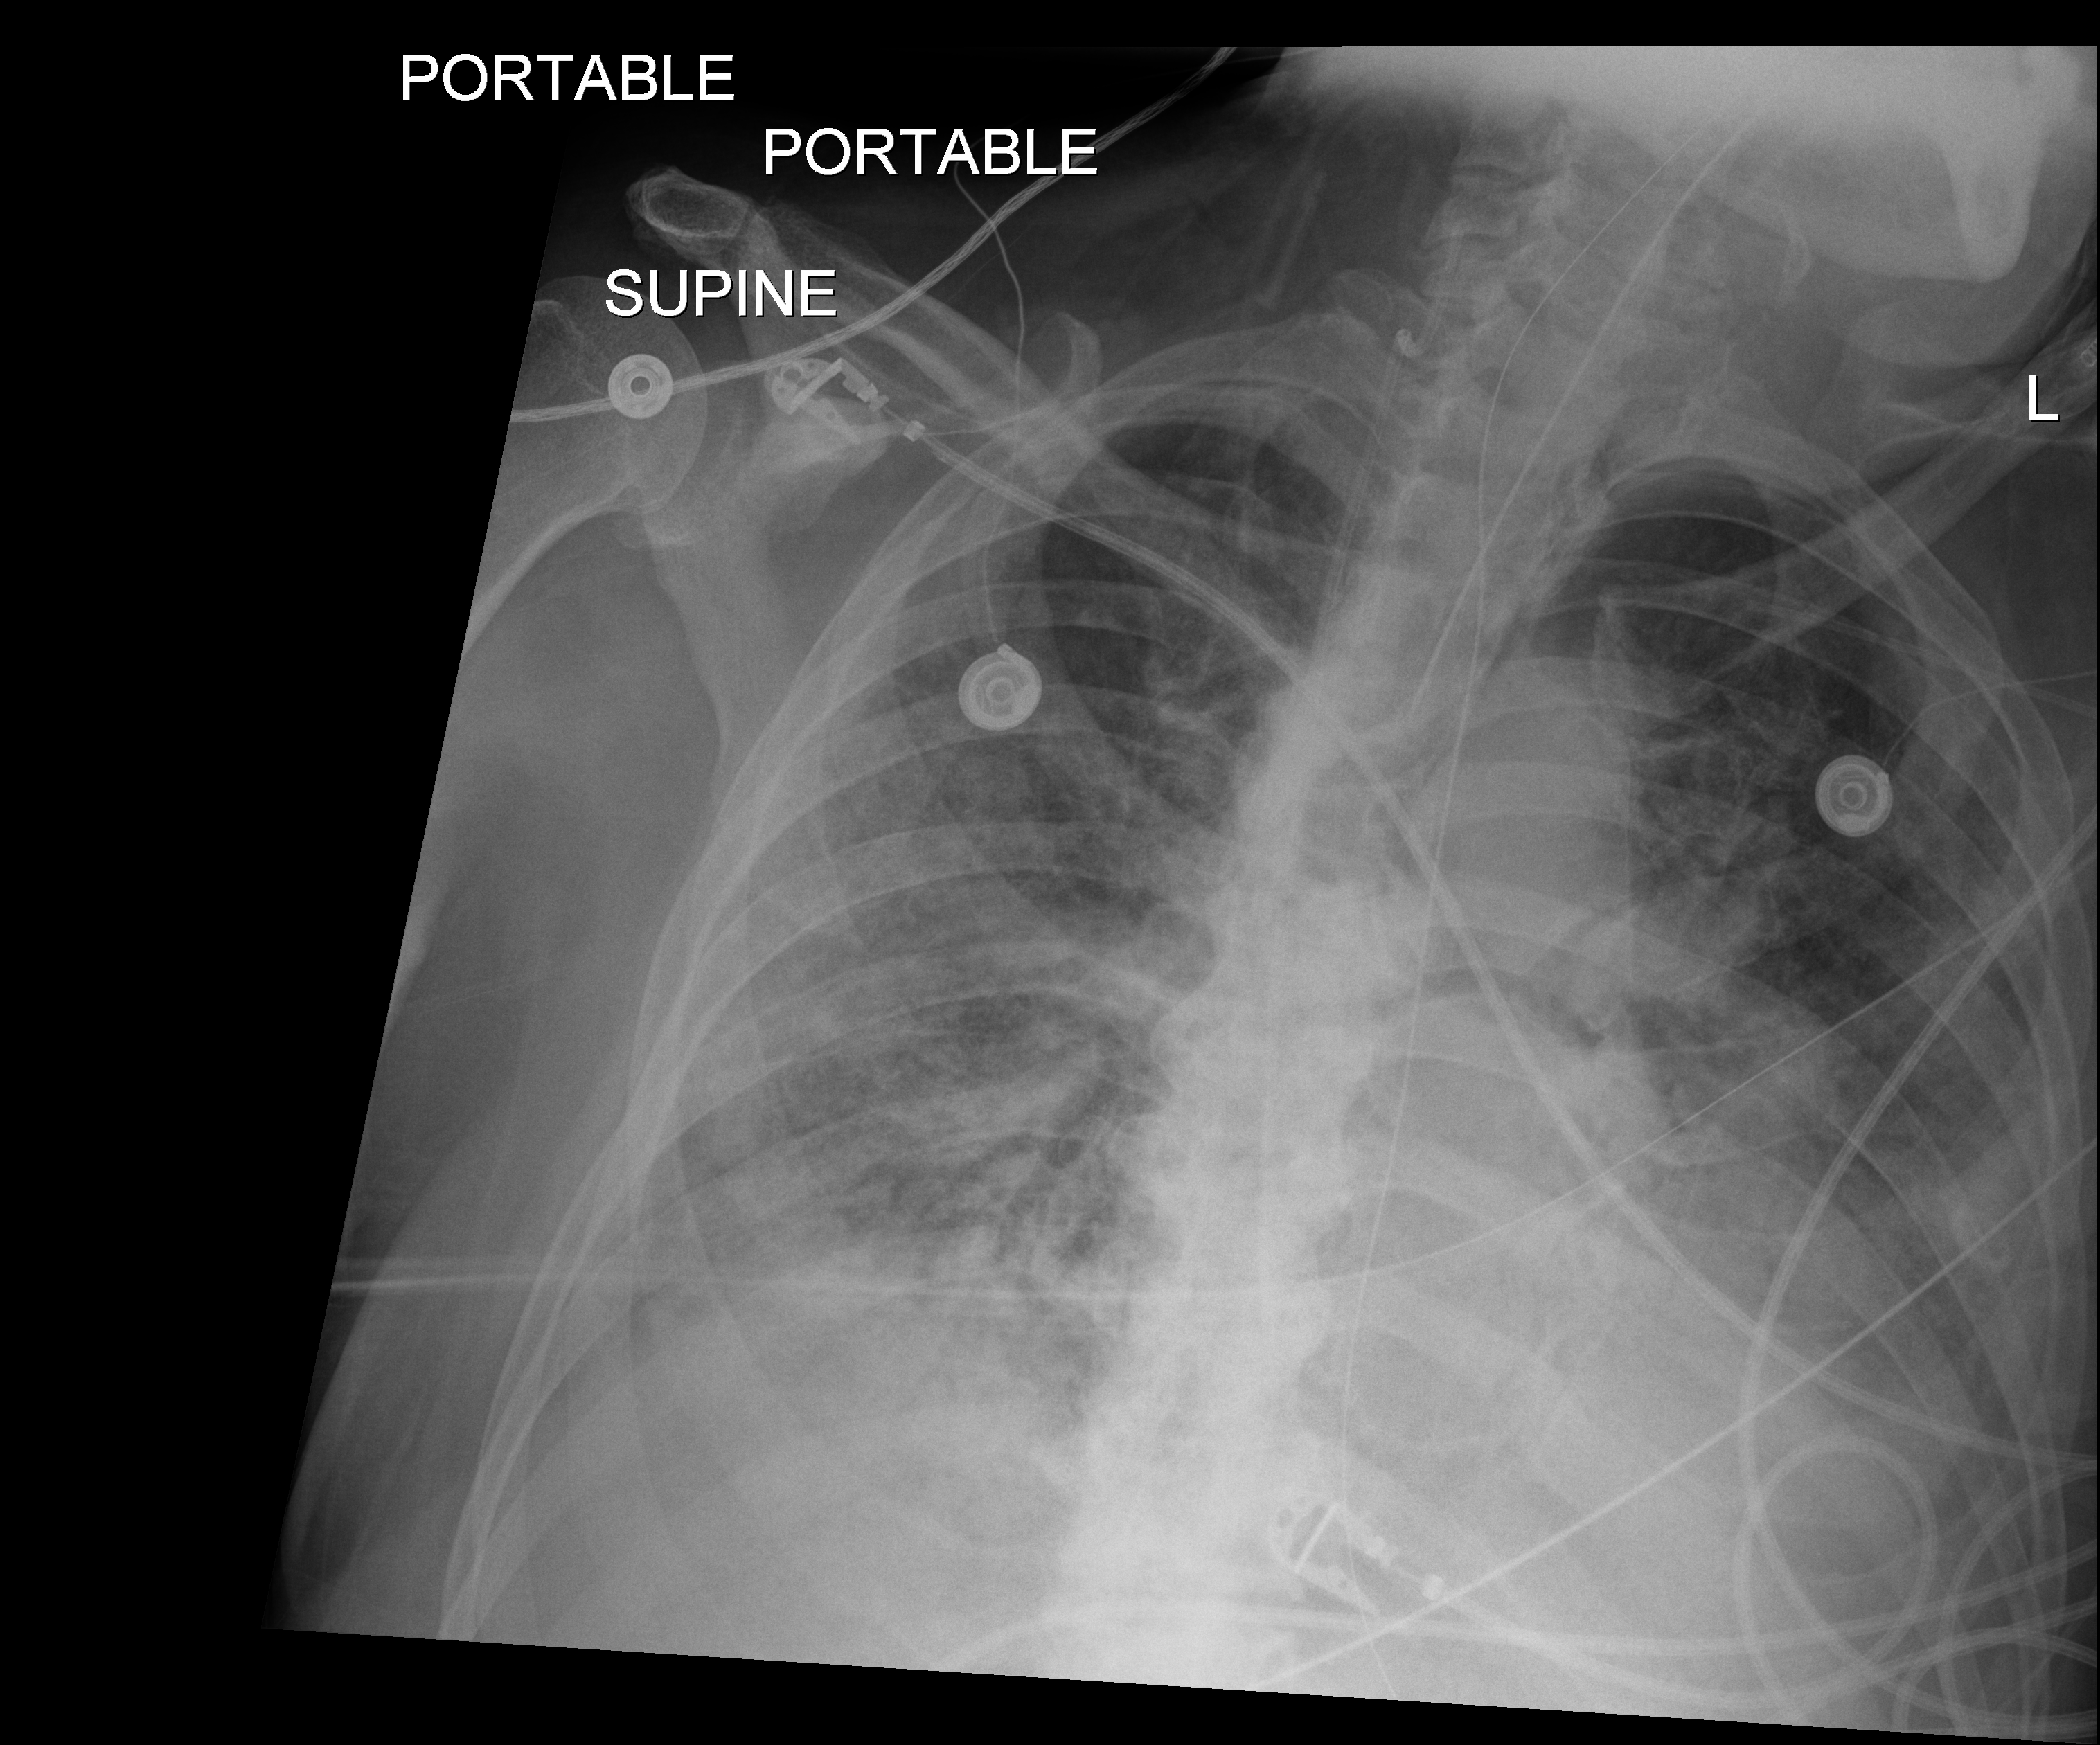
Portable chest radiograph, anteroposterior (AP) projection. Male patient hospitalised with COVID-19, age 75–90 years.
From the hospital-stay record, not from the radiograph (when in the stay this image was taken is not recorded): smoking status (admission record): former; other chronic lung disease (admission record): no.